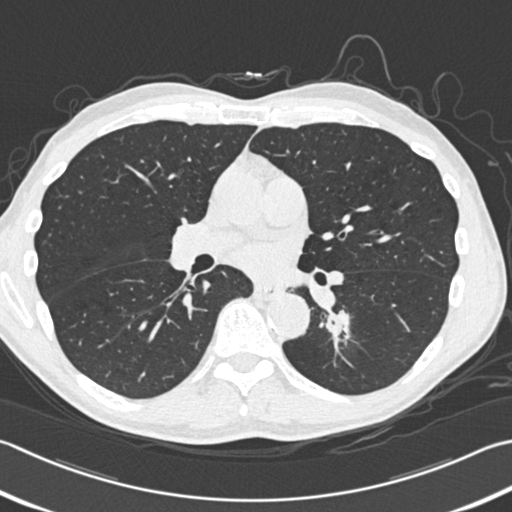
Low-dose screening chest CT, one axial slice; position 187 of 354 along the scan axis; 120 kVp; lung window (W 1500 / L -600 HU); 512 × 512 image matrix.
Structures marked on this image (expert manual segmentation):
- lesion 1 (tumor, lower lobe of left lung): bounding box (x1, y1, x2, y2) in pixels: (327, 310, 350, 335)